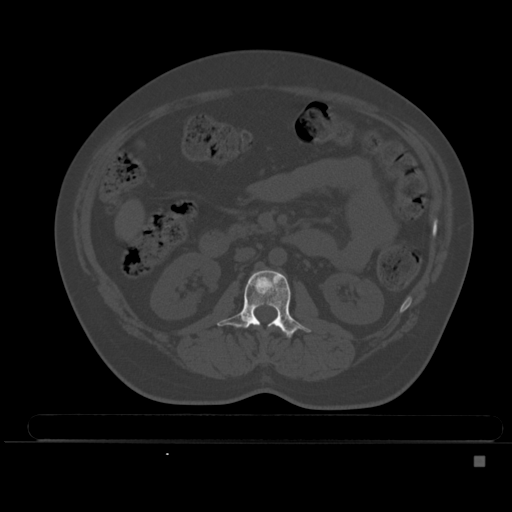
CT including the spine, one axial slice. Slice 176 of 495 in the series (ordered by position). Bone window (W 1800 / L 400 HU). 1.5 mm slice thickness. 512 × 512 image matrix, field of view 404 × 404 mm. Patient: female, 33 years. Case-level facts recorded for this patient, not image findings: primary cancer: breast.
Outlined on this slice (semi-automatic segmentation, software-assisted and operator-edited):
- L1 vertebra: box from (x=281, y=329) to (x=284, y=333) px
- L2 vertebra: (x=217, y=270)–(x=310, y=339)